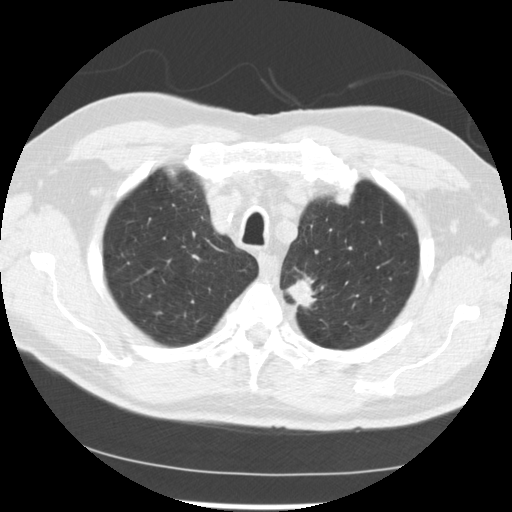
Axial slice from a low-dose chest CT screening exam, first (baseline) screen, lung window (W 1500 / L -600 HU), 2.5 mm slice thickness, 120 kVp, slice 206 of 249 in the series, 512 × 512 image matrix, field of view 341 × 341 mm. Male participant, aged 71 years at enrolment. Current smoker at enrolment.
Expert-annotated lung lesion, bounding box <272,267,336,318> (left, top, right, bottom; pixels). The screening reader recorded 2 non-calcified nodules or masses ≥4 mm on this exam (left upper lobe, left upper lobe); which of them this box marks is not recorded. Later outcome: lung cancer diagnosed 37 days after this screen — adenocarcinoma, NOS, left upper lobe, poorly differentiated (G3), stage IIIB (AJCC 6th edition), 25 mm at pathology.